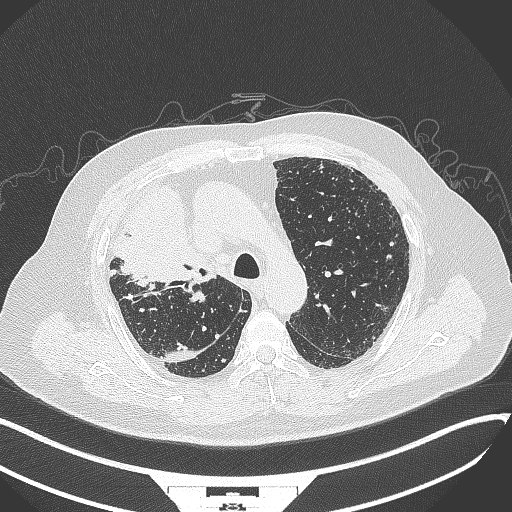
Chest CT, one axial slice; slice 251 of 384 in the series (ordered by position); lung window (W 1500 / L -600 HU); 1 mm slice thickness; 512 × 512 image matrix, field of view 400 × 400 mm. Male patient, age 69 years. Case-level facts recorded for this patient, not image findings: clinical TNM (as recorded): T4 N3 M1.
Annotated regions visible in this slice (bounding box drawn by a radiologist):
- lung tumour (recorded histology: adenocarcinoma): bounding box (x1, y1, x2, y2) in pixels: (120, 184, 212, 293)